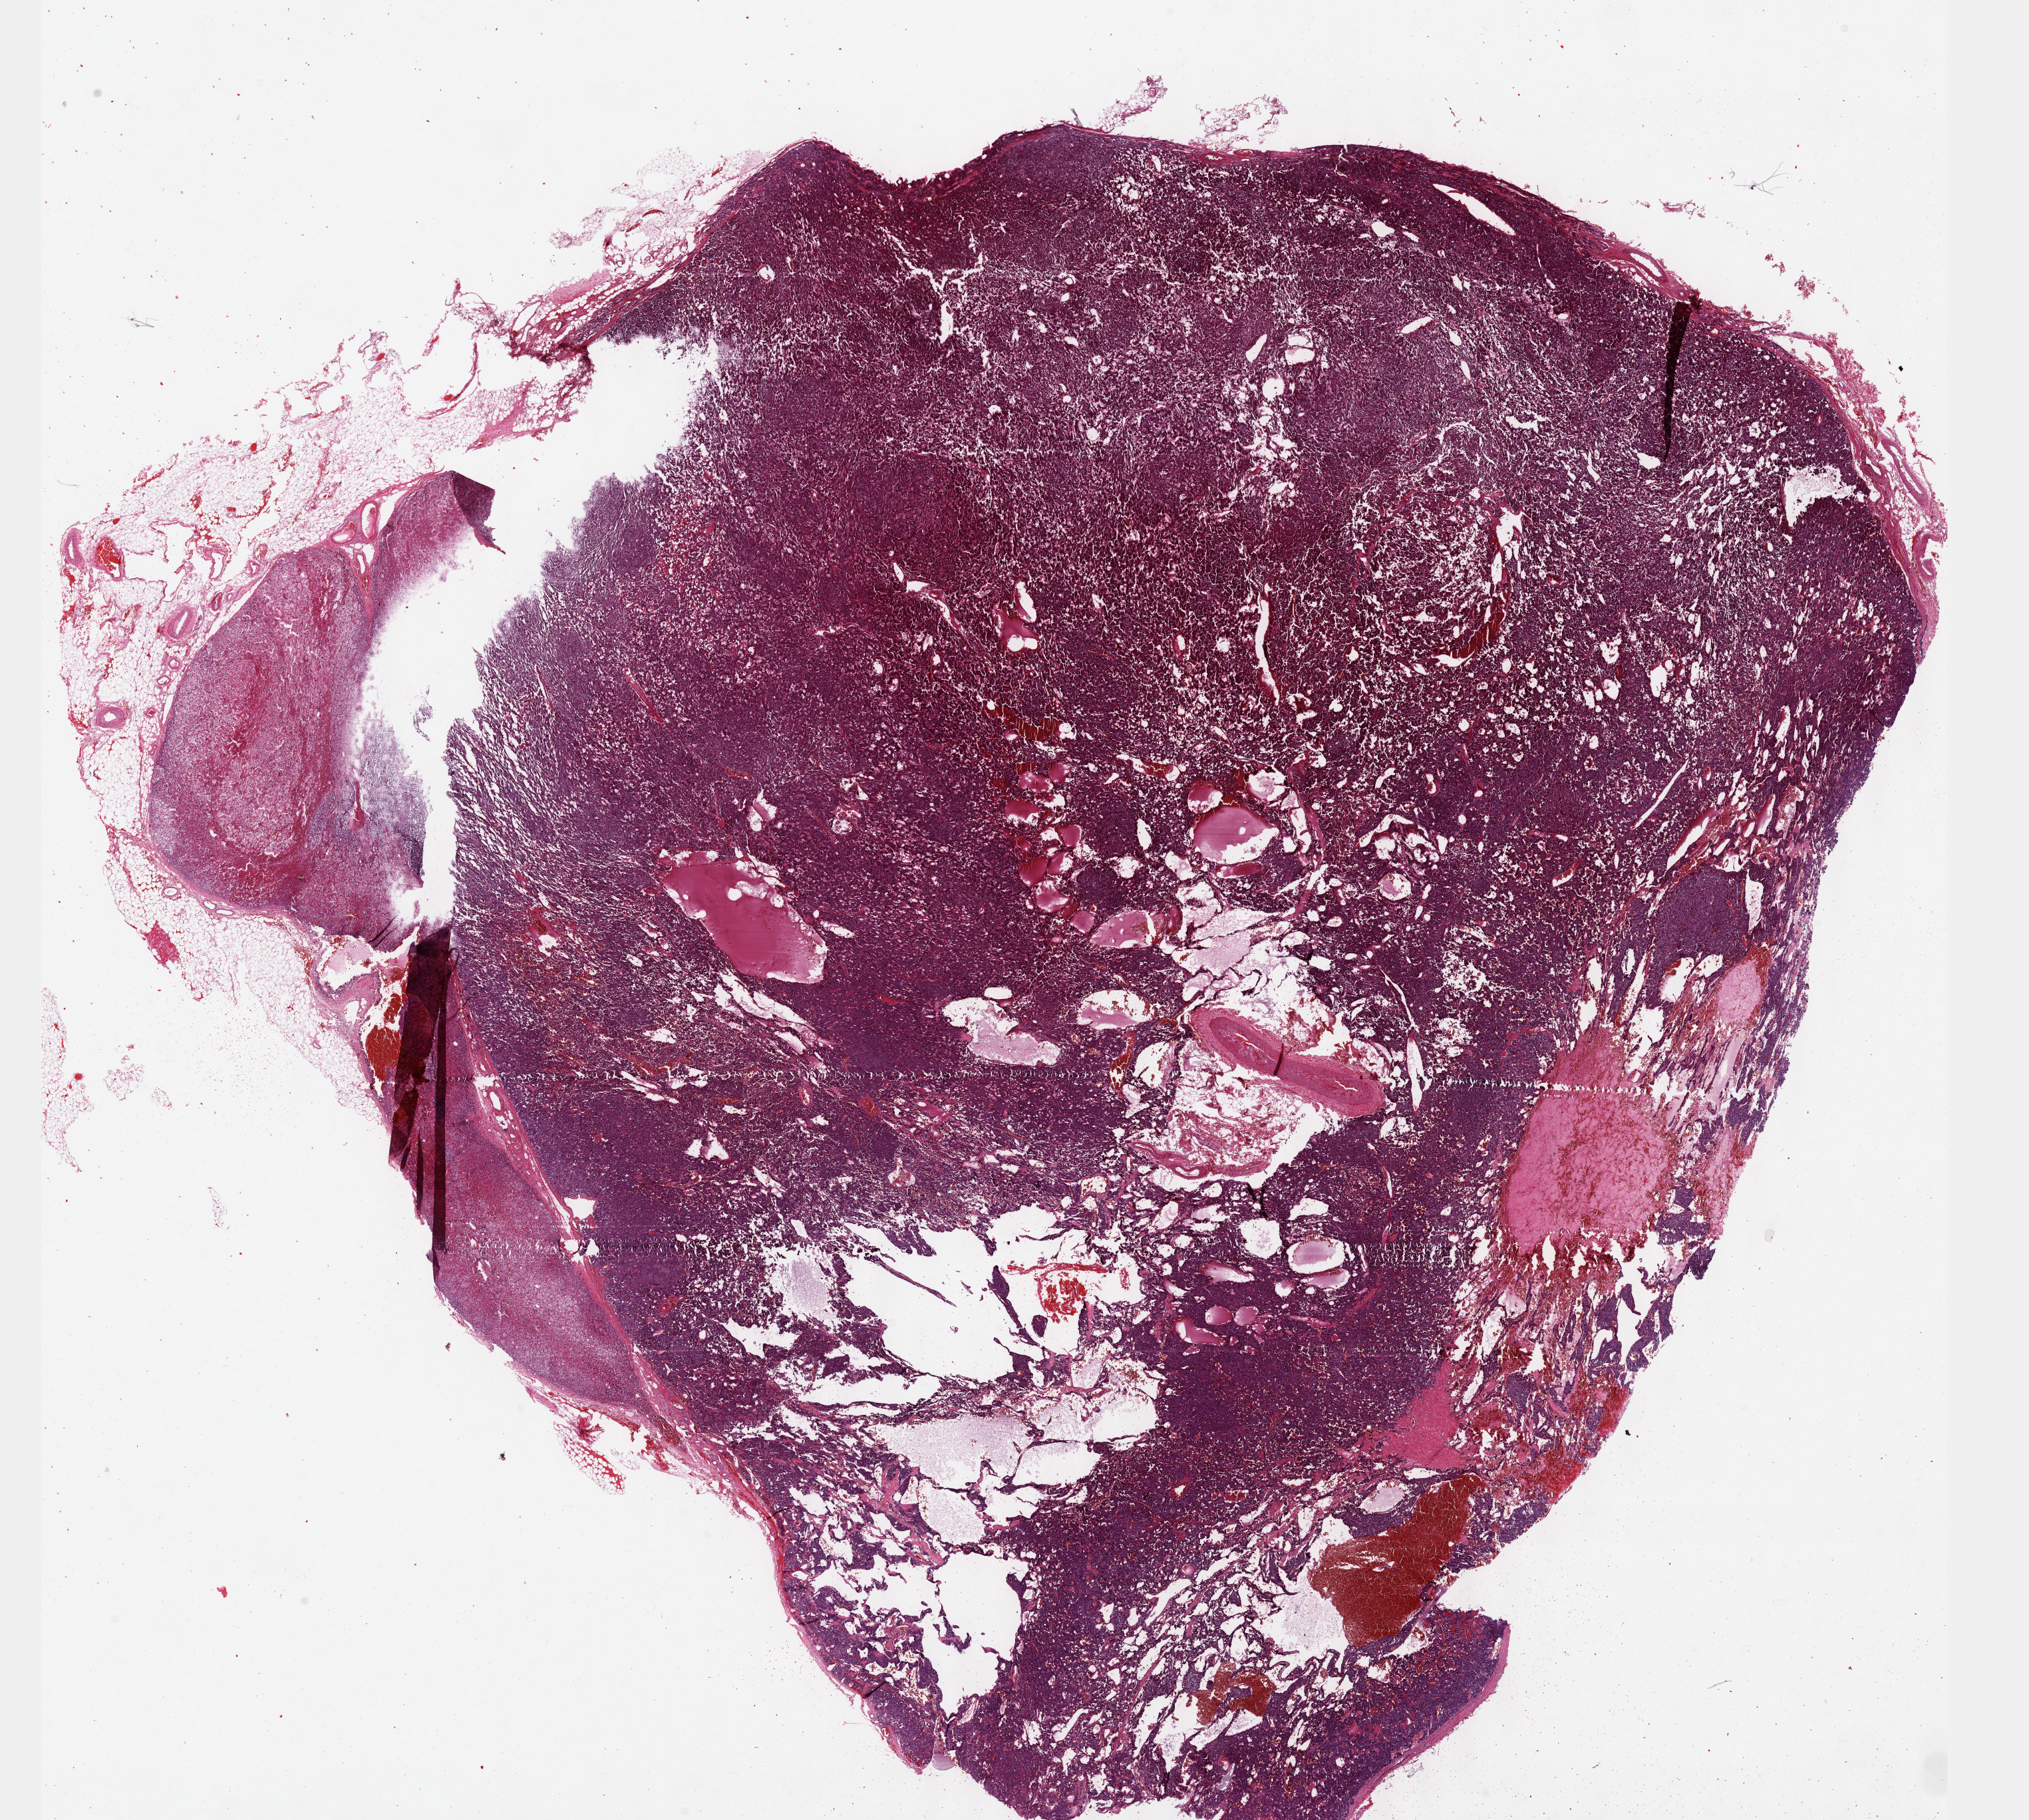
Digitized Hematoxylin and eosin (H&E) stained tissue section (whole slide), shown as a low-resolution overview of the whole scanned area (about 24.6 x 22.1 mm); formalin-fixed paraffin-embedded (FFPE) diagnostic section; sample: primary tumour, adrenal gland. Female patient; age at initial diagnosis 73 years.
* laterality: left
* histologic diagnosis: Pheochromocytoma, NOS